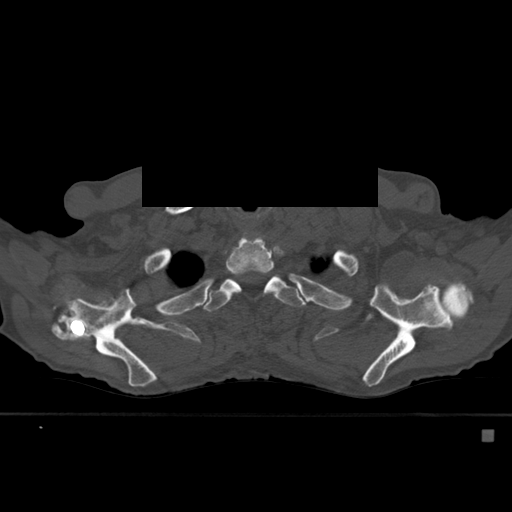
CT including the spine, one axial slice; slice 440 of 527 in the series (ordered by position); bone window (W 1800 / L 400 HU); 512 × 512 image matrix, field of view 373 × 373 mm. Male patient, age 78 years. Case-level facts recorded for this patient, not image findings: primary cancer: prostate.
Structures marked on this image (semi-automatic segmentation, software-assisted and operator-edited):
- T2 vertebra: bounding box <225,236,279,297> (left, top, right, bottom; pixels)
- T3 vertebra: <203,271,302,312>